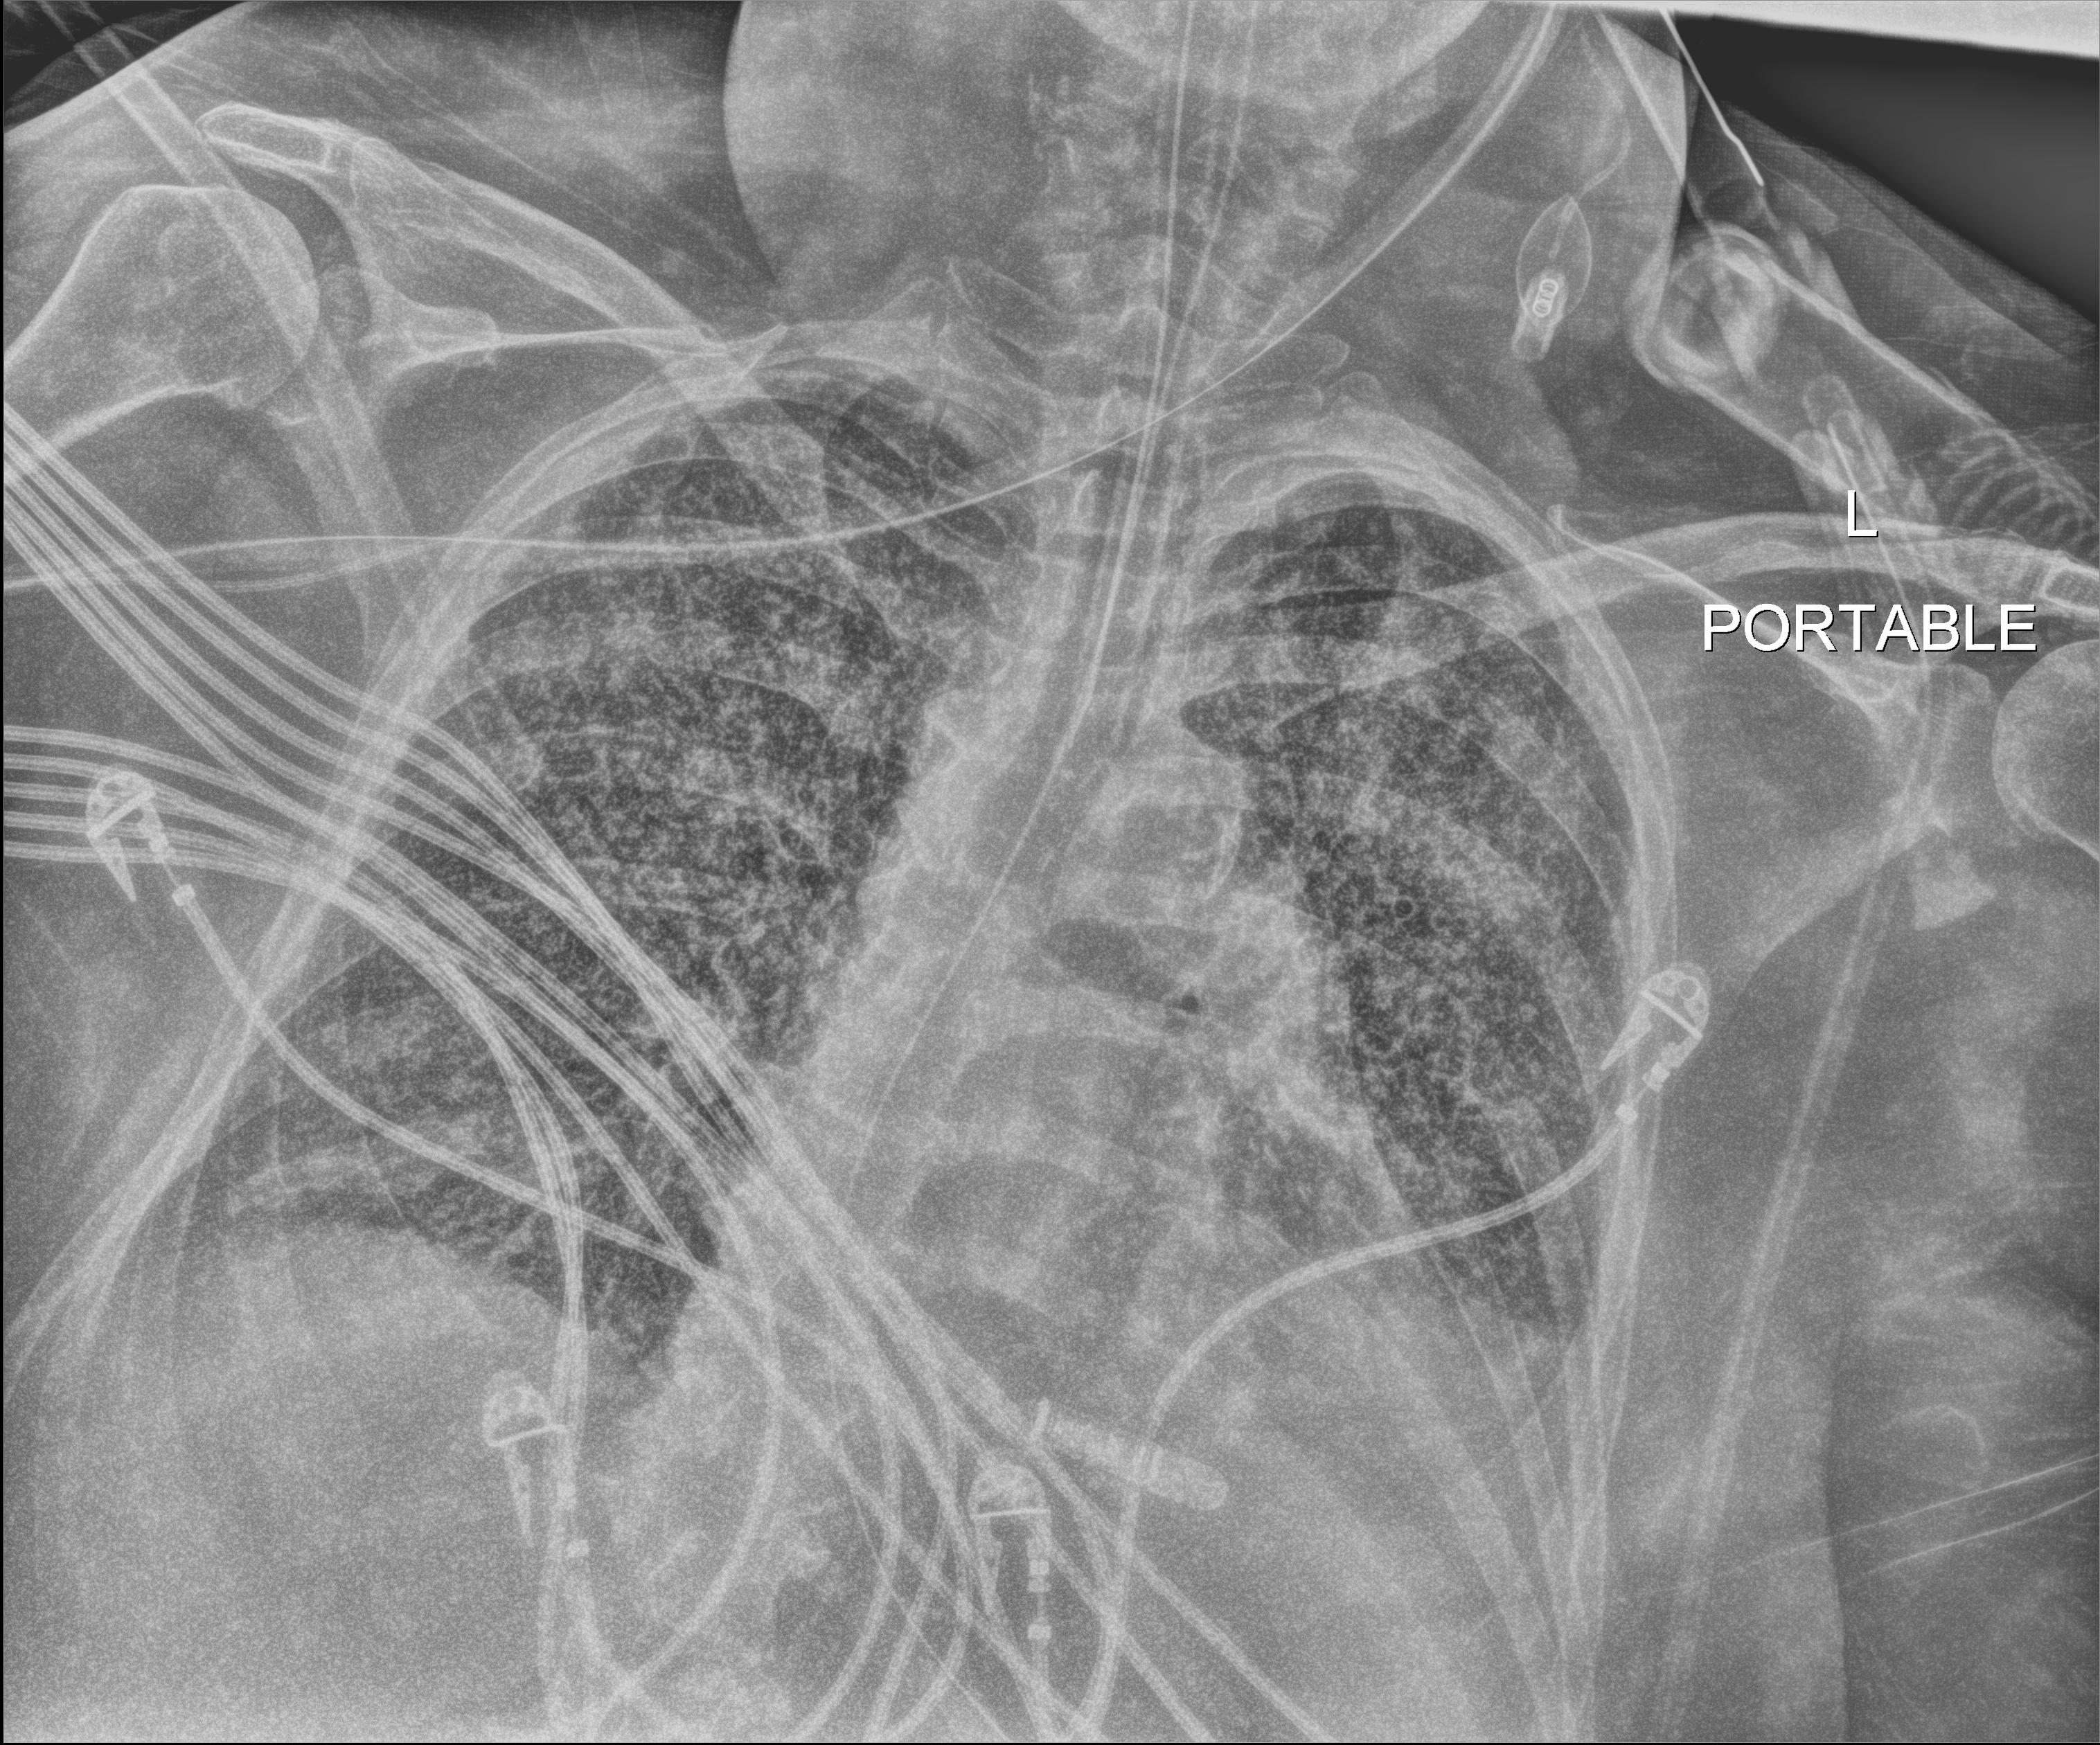
Portable chest radiograph, anteroposterior (AP) projection. Patient hospitalised with COVID-19; female, aged 60–74 years.
Hospital-stay facts (about this admission, not read from this image; timing relative to this image not recorded): mechanically ventilated during this hospital stay: yes; admitted to intensive care during this hospital stay: yes.